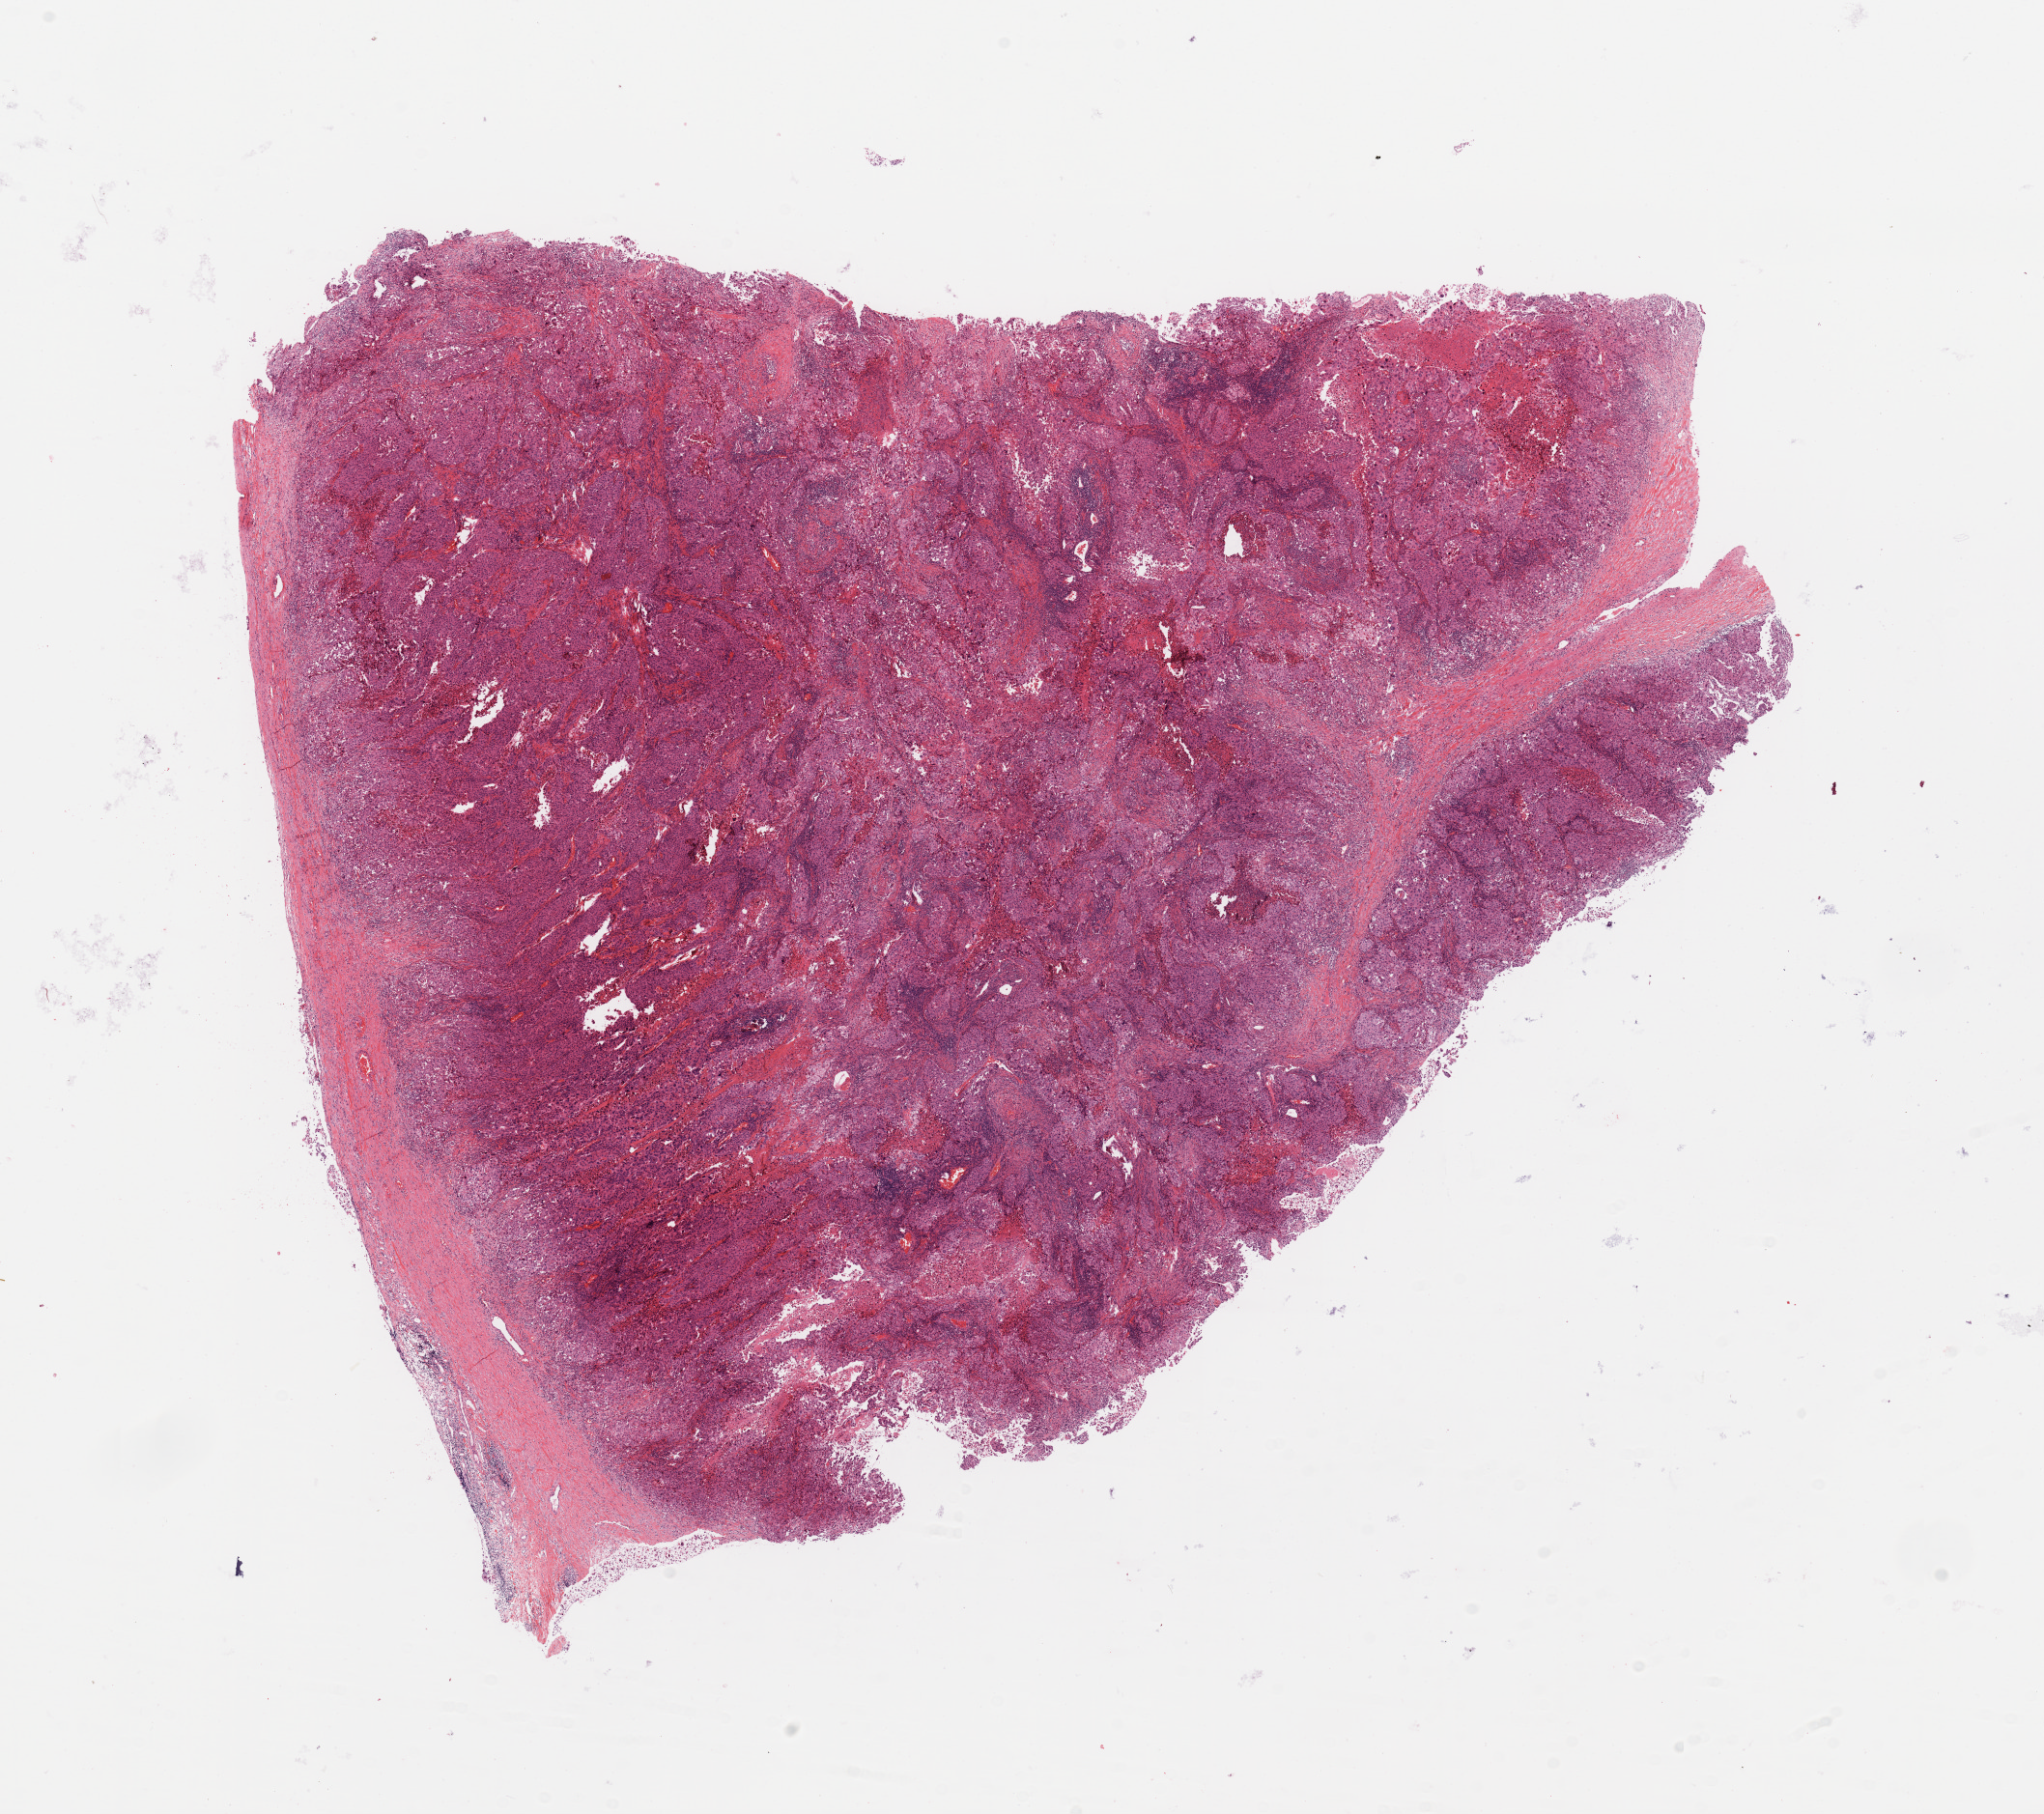
Digitized H&E tissue section (whole slide), shown as a low-resolution overview of the whole scanned area (about 16.7 x 14.9 mm), tumour tissue sample, sampled site: lung. Patient: male, age 56 years. Histologic grade: G3 (poorly differentiated). Slide review estimates, as recorded: tumour nuclei 80%, necrosis 10%.
Primary tumour site (as recorded): right lower lobe. AJCC pathologic stage: IIIA. Diagnosis: Adenocarcinoma, NOS.